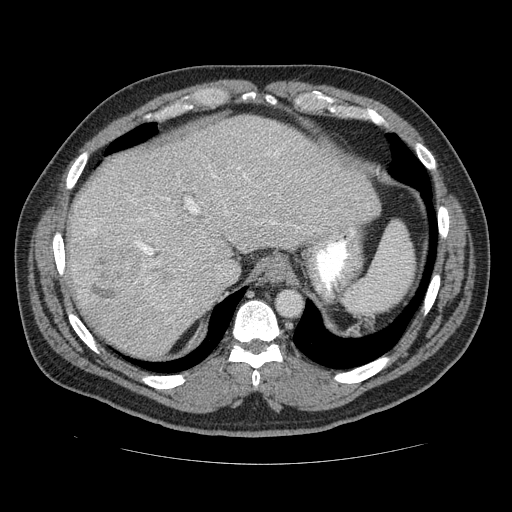
Contrast-enhanced abdominal CT (liver protocol), one axial slice; position 97 of 113 along the scan axis; reconstruction kernel STANDARD; soft-tissue window (W 400 / L 40 HU); 512 × 512 image matrix, field of view 400 × 400 mm. Case-level facts recorded for this patient, not image findings: diagnosis: hepatocellular carcinoma (patient treated with transarterial chemoembolisation; whether this scan precedes or follows treatment is not stated here); TNM stage (as recorded): Stage-II; Child-Pugh class: B; tumour differentiation: moderately differentiated; tumour nodularity: multinodular.
Outlined on this slice (semi-automatically segmented with operator editing):
- abdominal aorta: bounding box <278,291,301,315> (left, top, right, bottom; pixels)
- liver parenchyma outside the tumour (the mass and vessels are separate outlines, so this box may not span the whole liver): <62,117,382,354>
- mass: <74,211,179,309>
- liver vessels: <141,185,263,302>